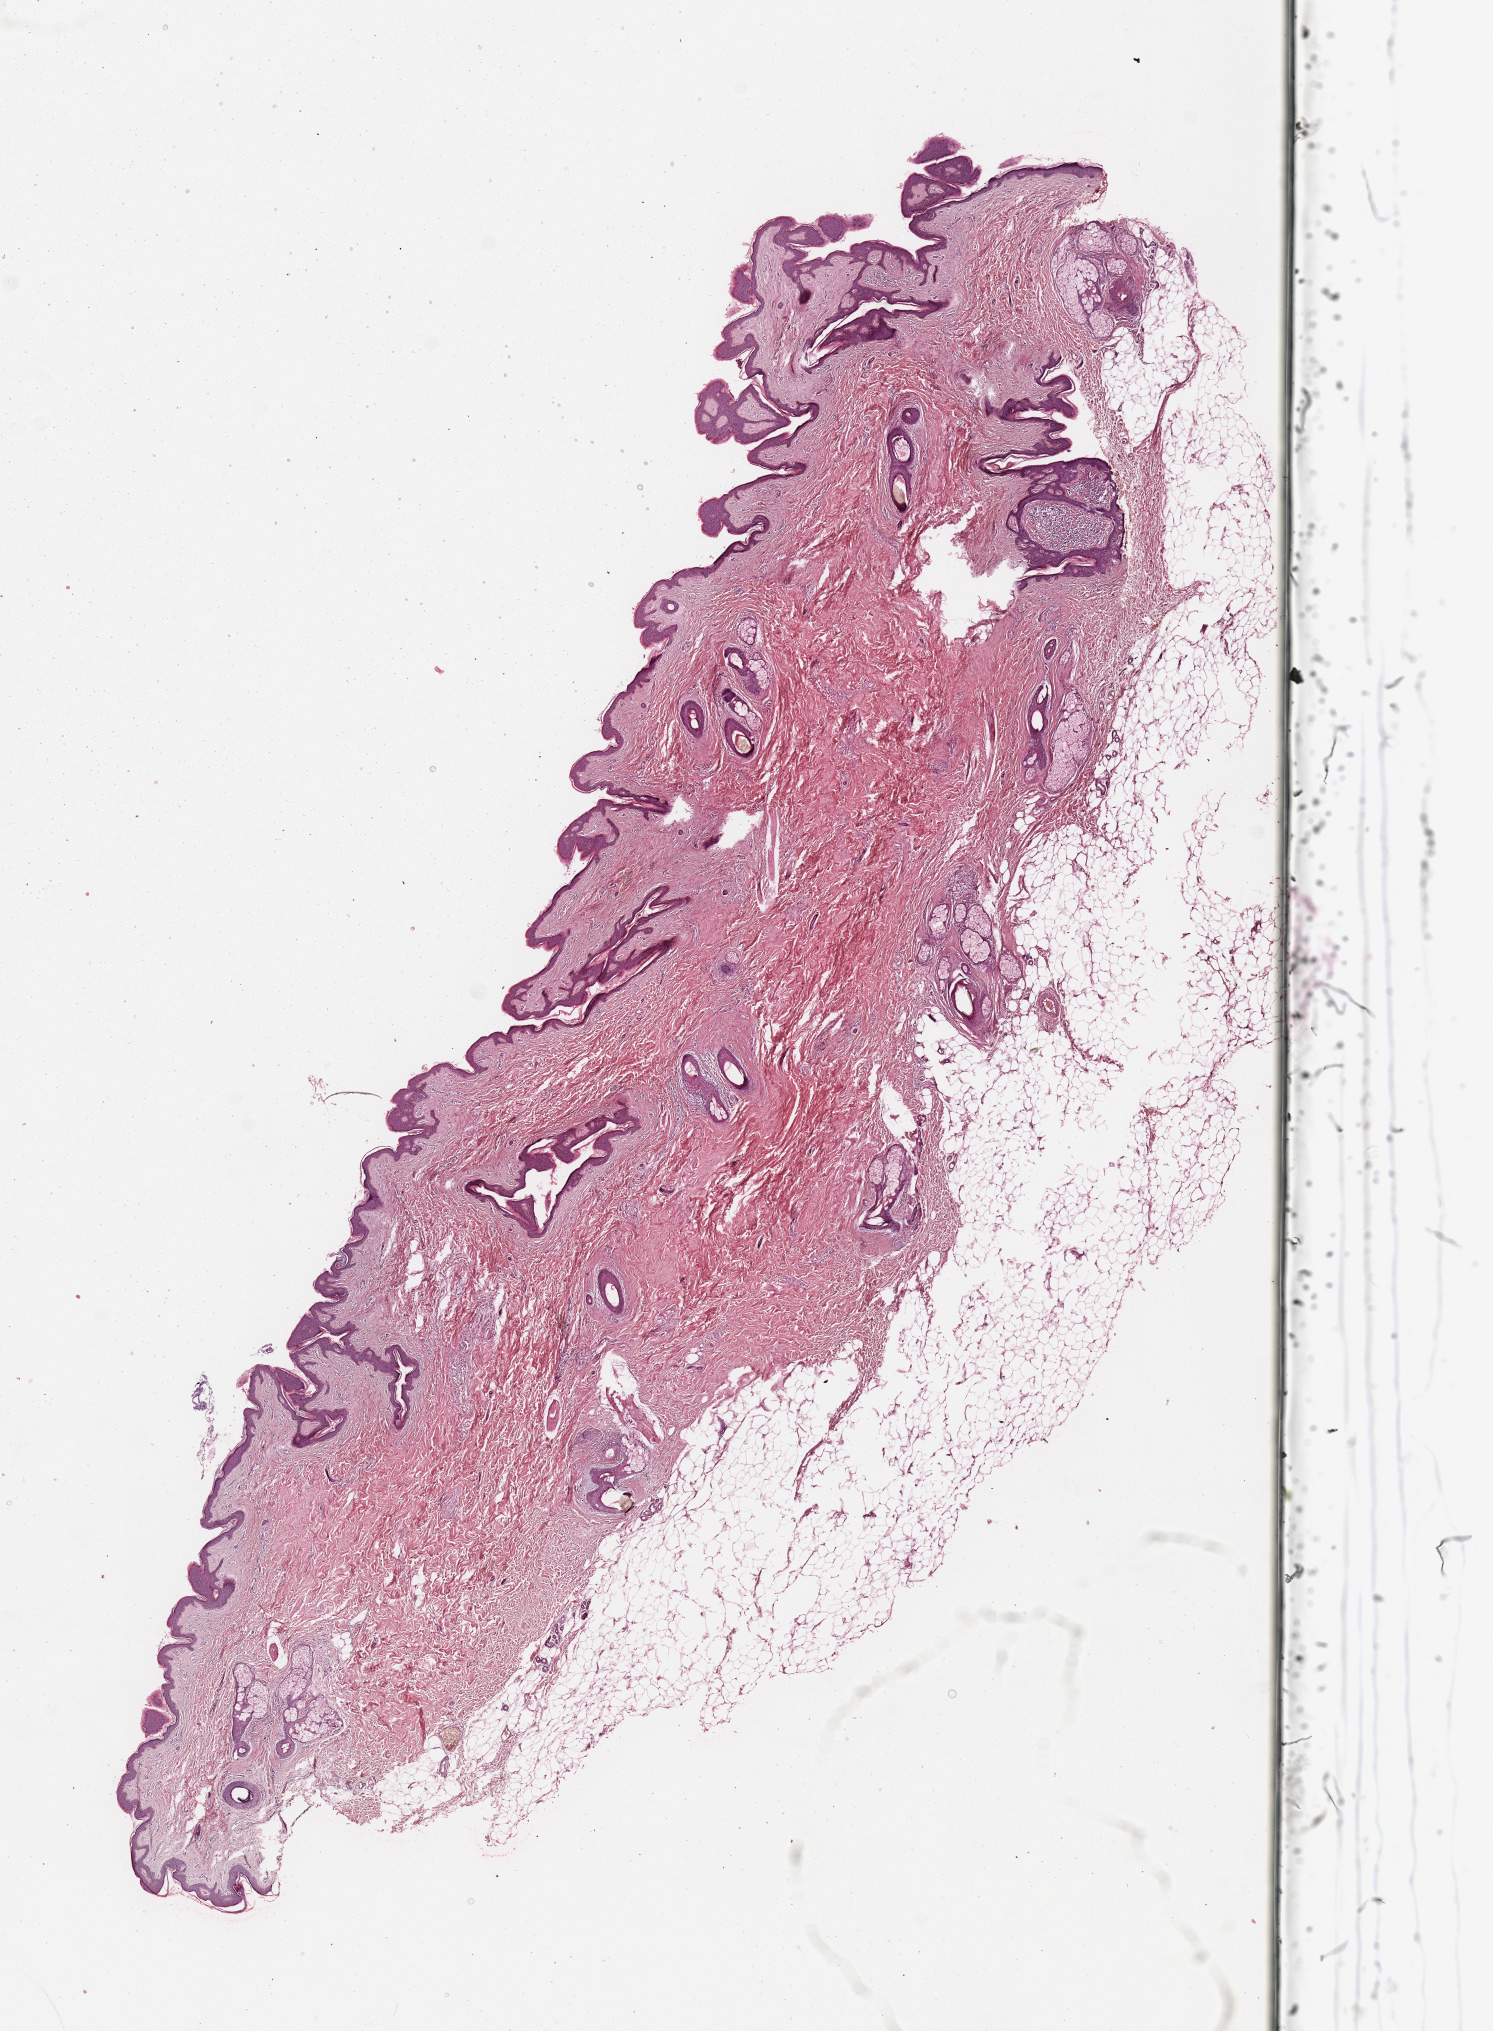
H&E-stained whole-slide image — low-resolution overview of the scanned area, about 11.8 x 16.1 mm (from a 20x scan); normal (non-tumour) tissue sample, sampled site: lymph node. 68-year-old female patient.
This section: normal (non-tumour) tissue from the same patient. Patient diagnosis: Malignant melanoma, NOS.